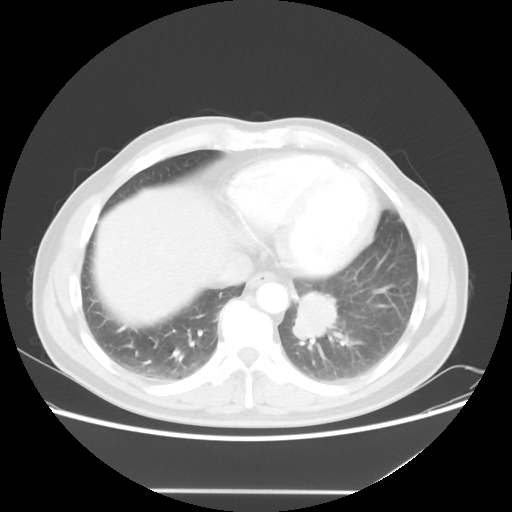
Chest CT, one axial slice. Position 18 of 56 along the scan axis. Reconstruction kernel STANDARD. Lung window (W 1500 / L -600 HU). 512 × 512 image matrix, field of view 385 × 385 mm. Patient: male, 61 years. Case-level facts recorded for this patient, not image findings: clinical TNM (as recorded): T1c N0 M0.
Annotated regions visible in this slice (bounding box drawn by a radiologist):
- lung tumour (recorded histology: adenocarcinoma): bounding box [x1, y1, x2, y2] px = [284, 283, 345, 353]